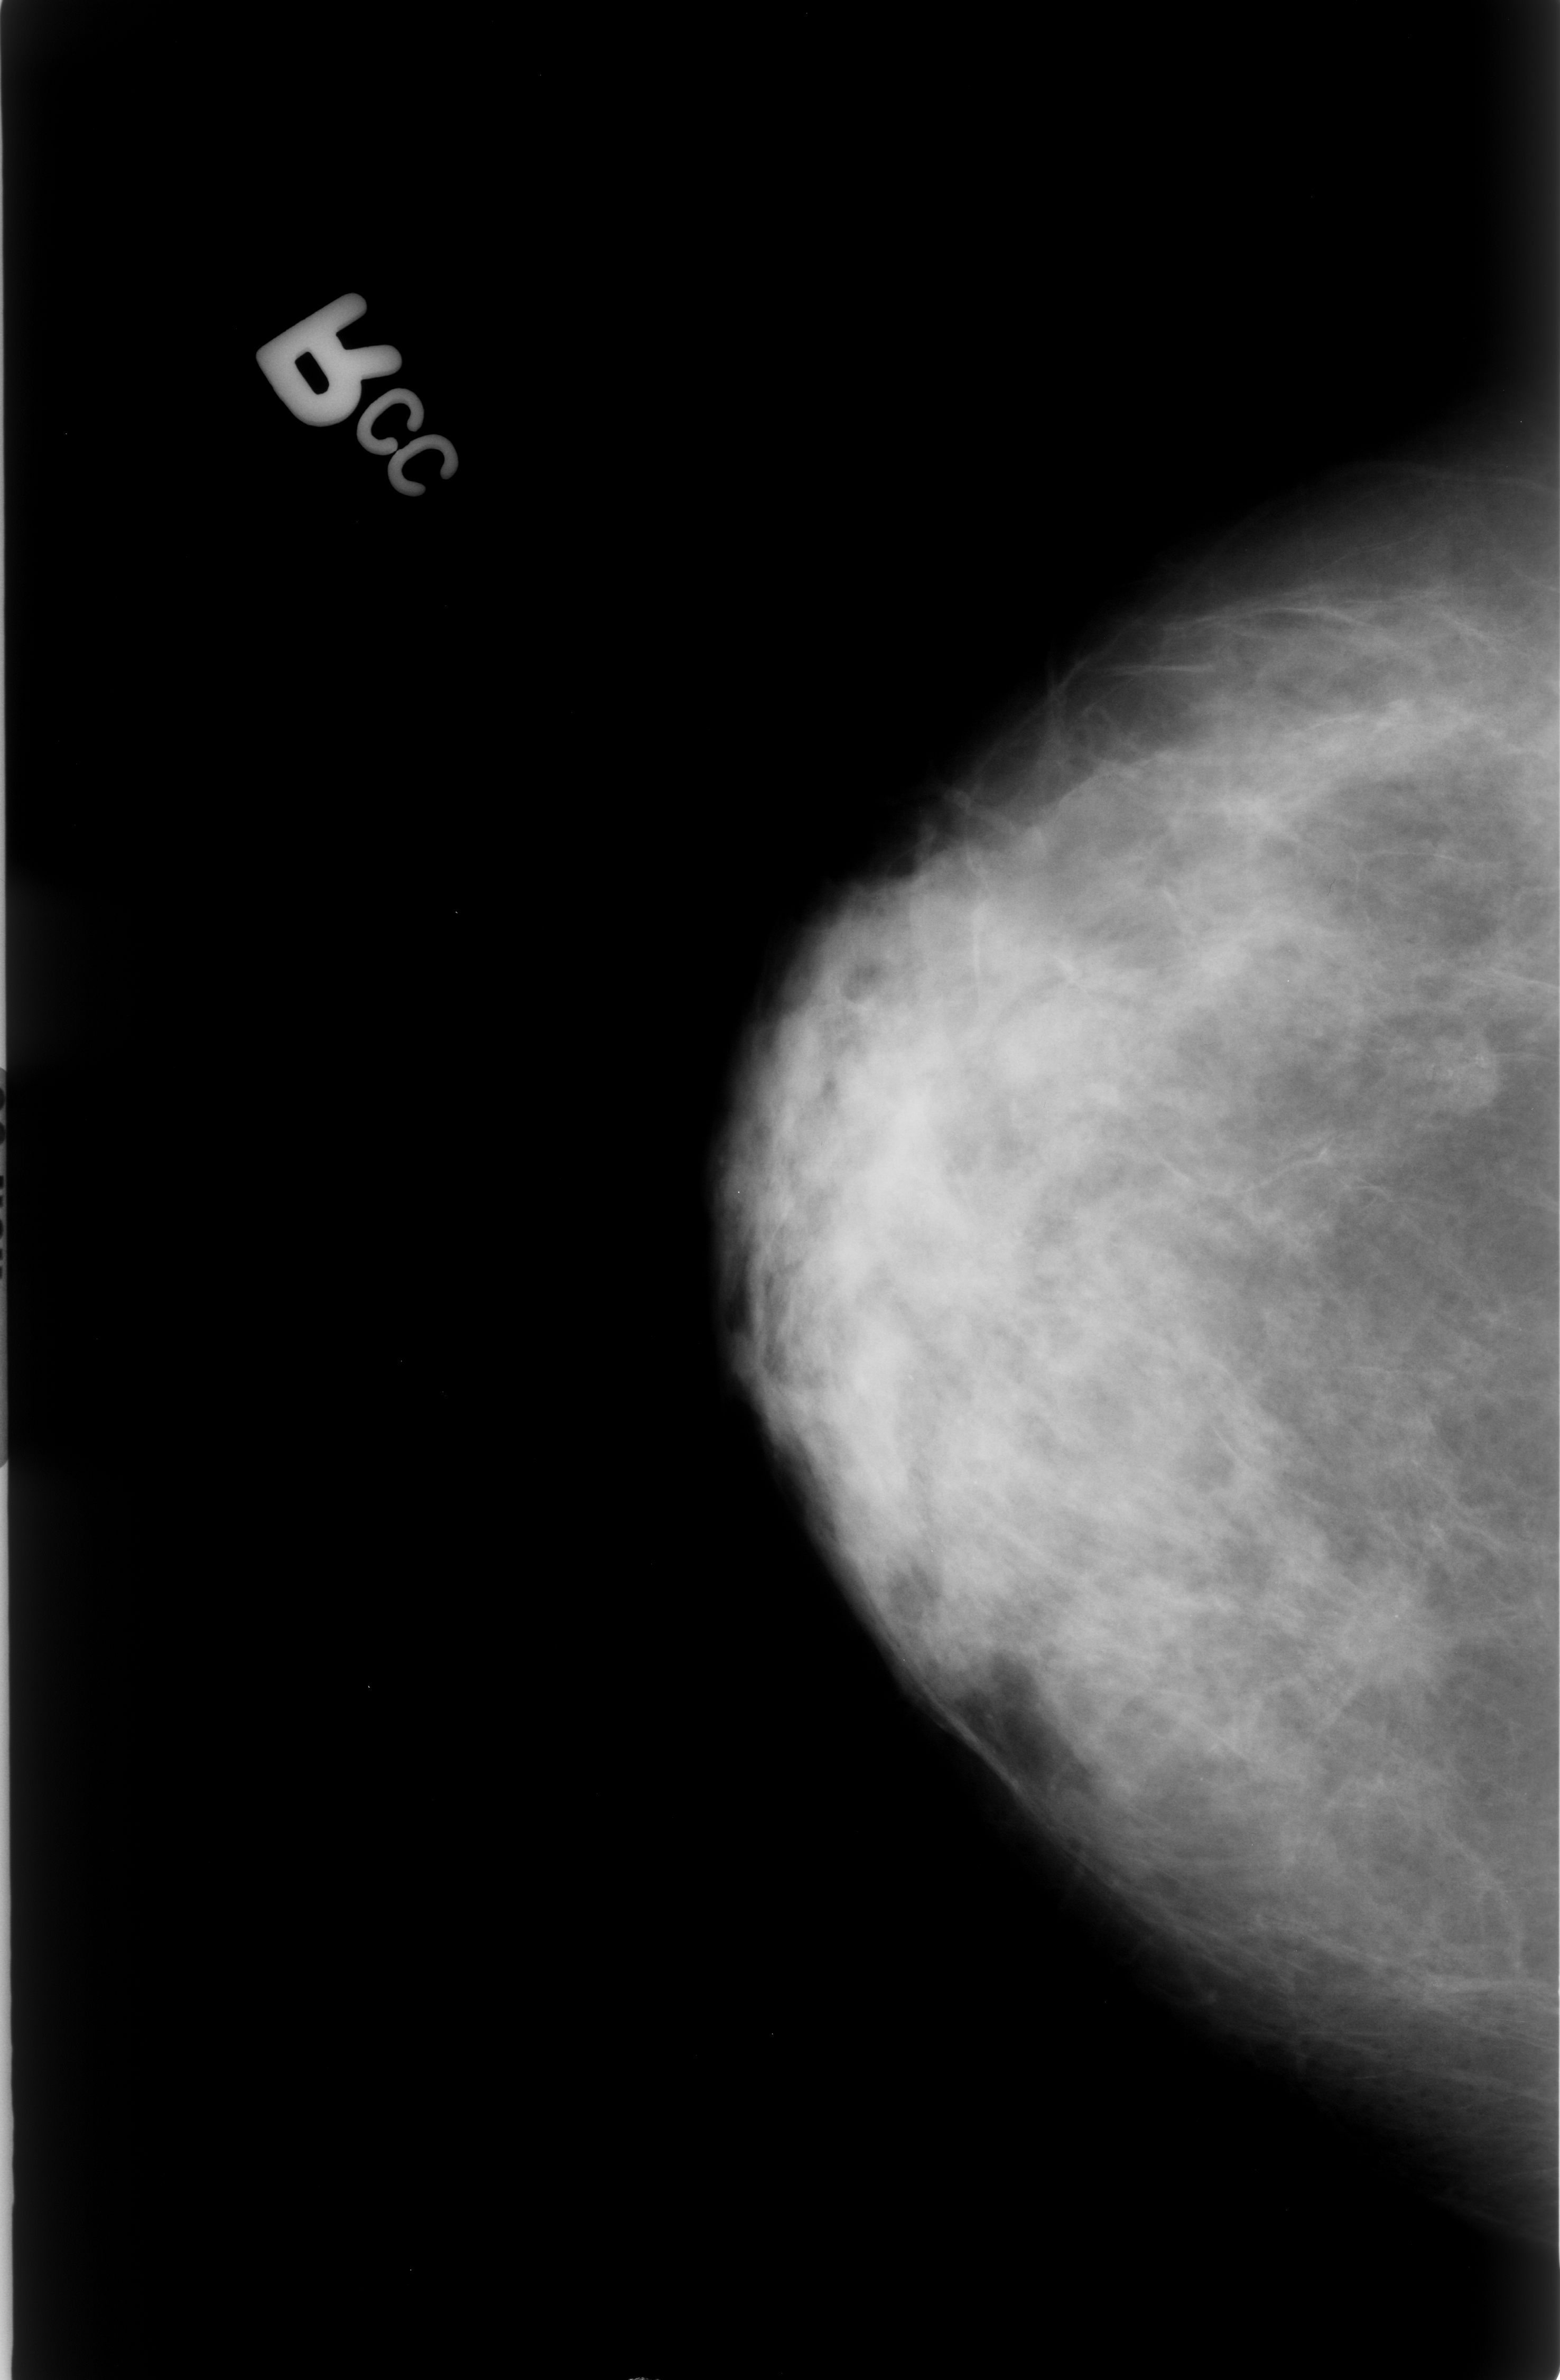
Scanned film-screen mammogram; right breast; craniocaudal (CC) view; BI-RADS breast density category 3 (scale 1–4); 1560 × 2380 image matrix.
Marked abnormalities (boxes around the expert regions of interest):
- calcifications, morphology punctate, distribution clustered; BI-RADS assessment category 4; pathology (as recorded): malignant: bounding box <1272,1513,1544,1751> (left, top, right, bottom; pixels)